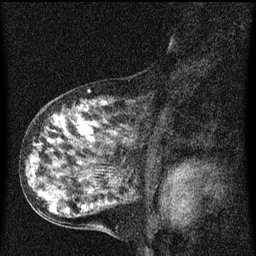
Breast MRI (dynamic contrast-enhanced), one sagittal slice. Position 29 of 60 along the scan axis. Dynamic contrast-enhanced series, image 2 of 3 at this slice position (ordered by acquisition). 1.5 T. TE 4.2 ms, TR 8 ms. 2 mm slice thickness. 256 × 256 image matrix, field of view 180 × 180 mm. Patient: female, 55 years.
Outlined on this slice (semi-automatically segmented with operator editing):
- analysis volume of interest (the breast-tissue region the enhancement analysis was run in; not a lesion): bounding box (x1, y1, x2, y2) in pixels: (38, 92, 175, 159)
- tumour enhancement mask (voxels above the 70 % enhancement threshold inside the analysis volume of interest): (54, 114, 97, 143)